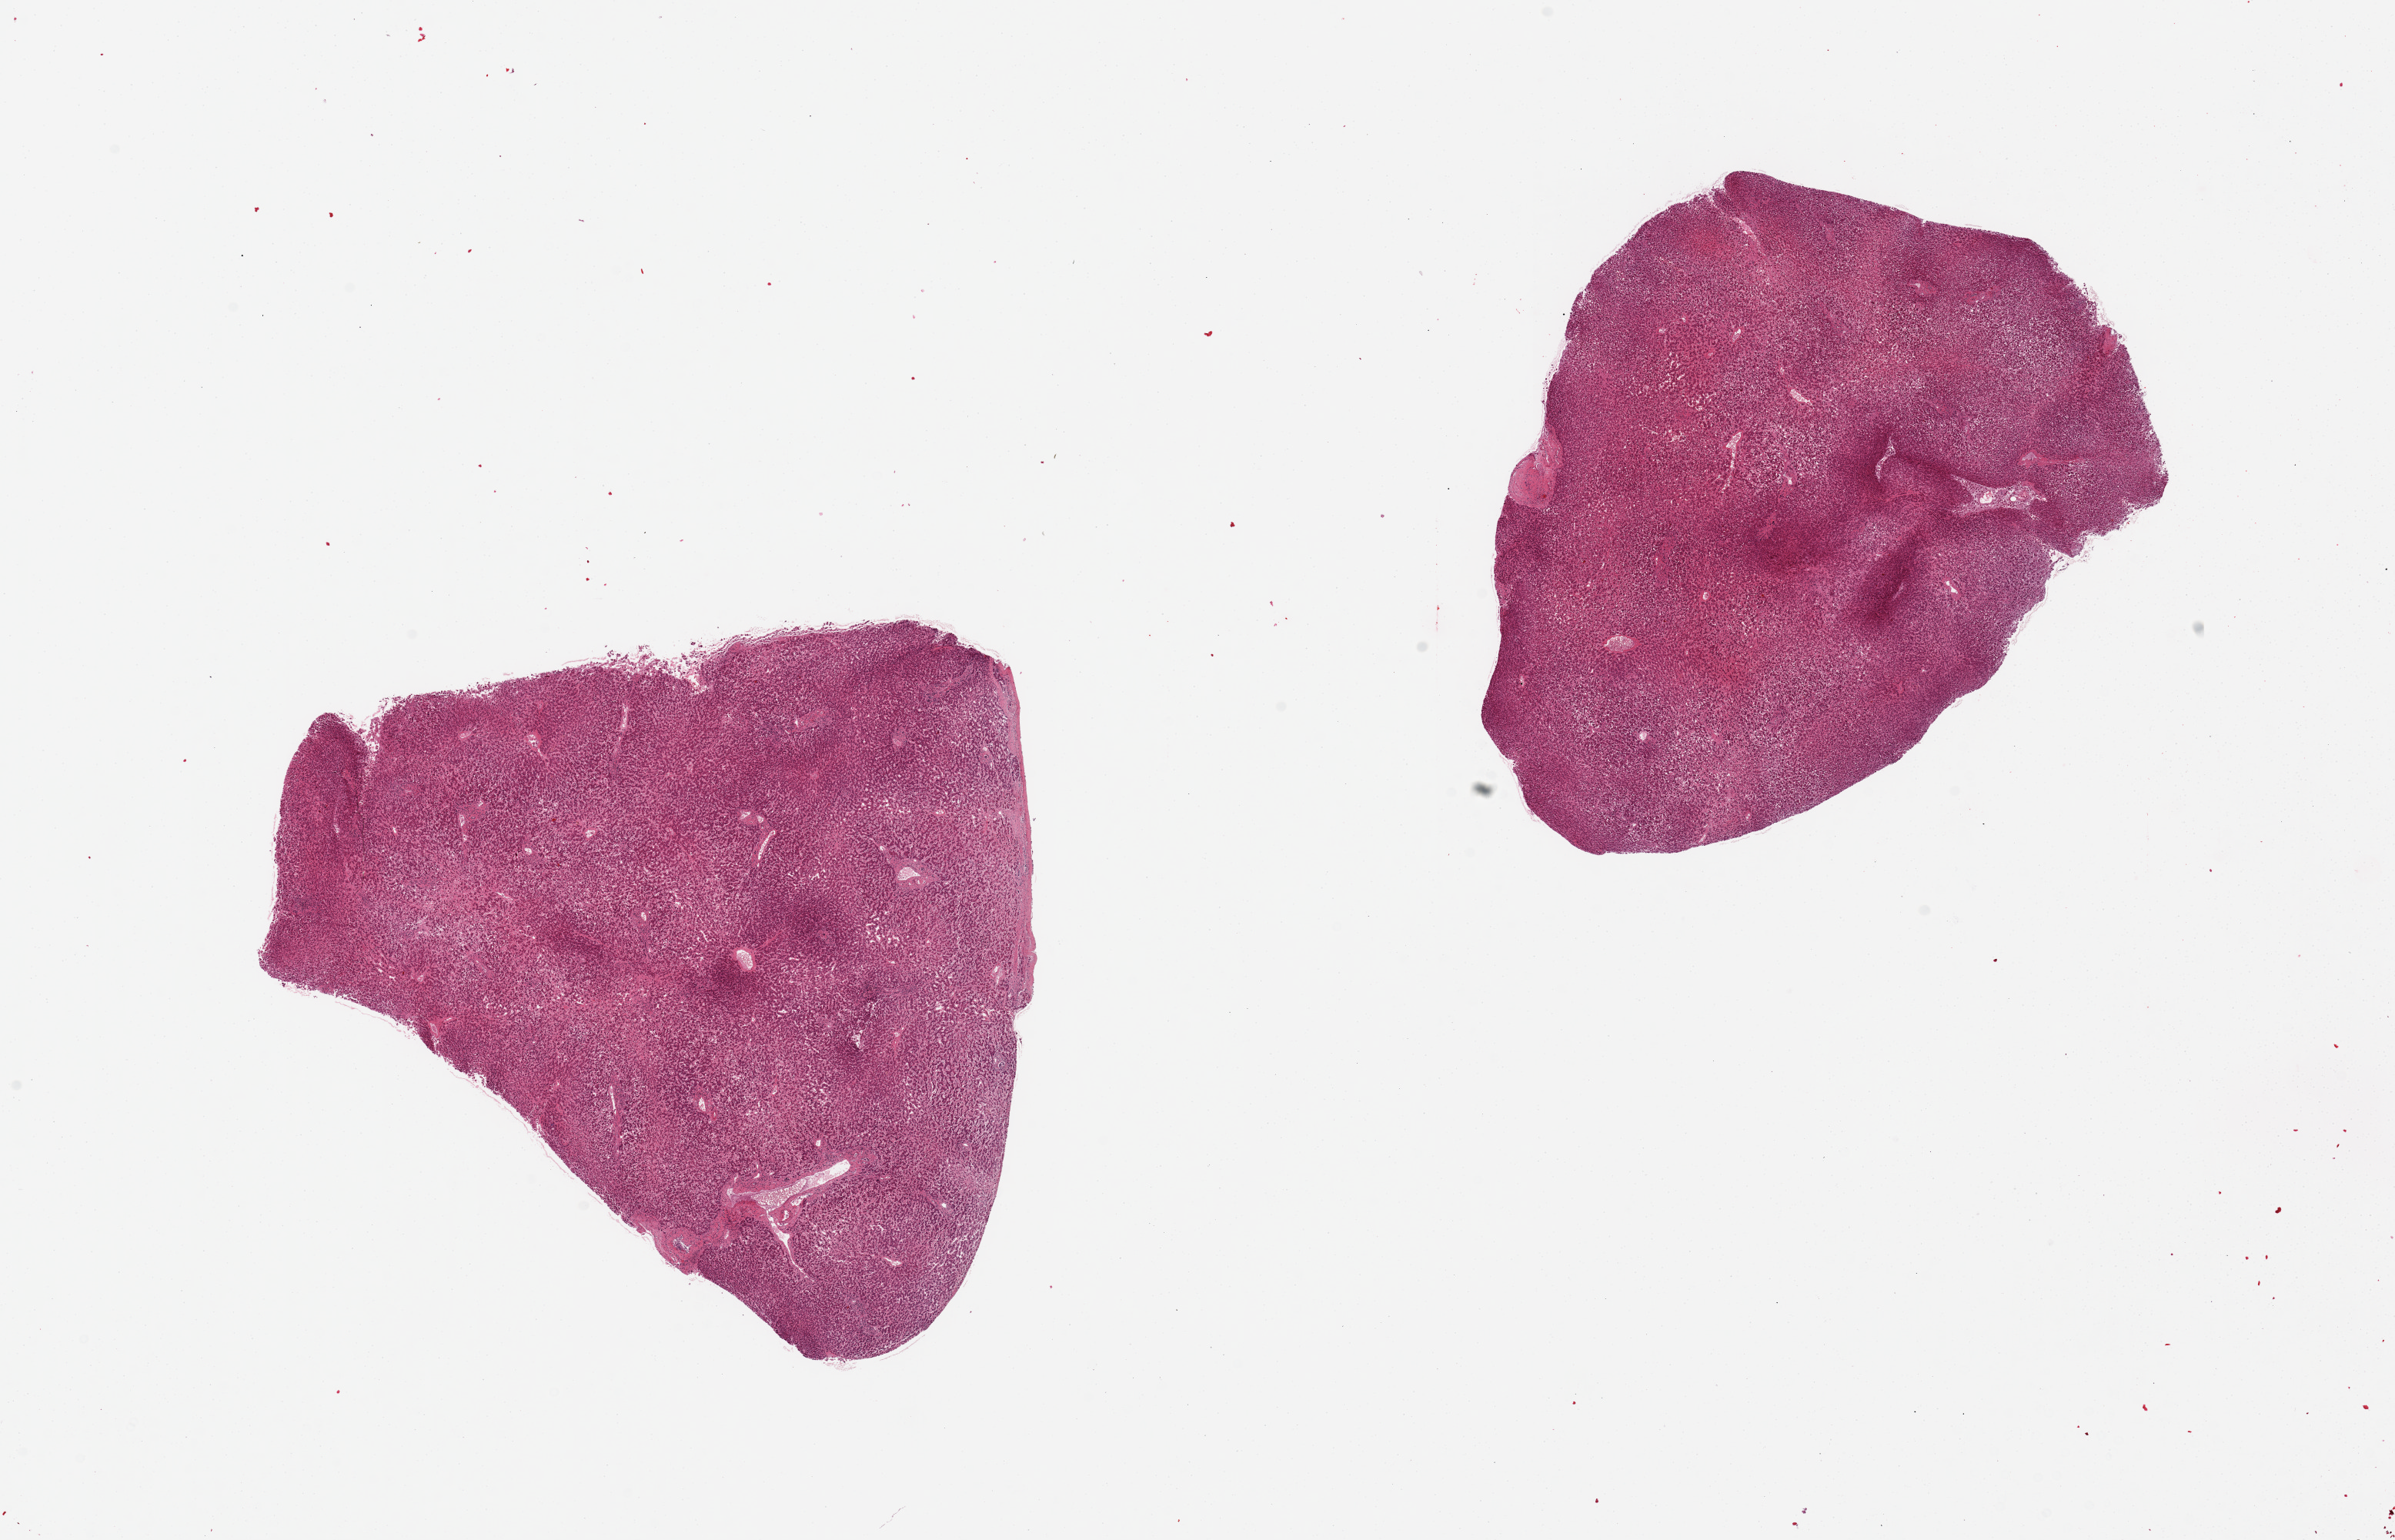
Whole-slide image, H&E stain — whole scanned area (about 24.6 x 15.8 mm, slide scanned at 20x) shown as a low-resolution overview, PAXgene-fixed paraffin-embedded (PFPE) section, sampled site (target tissue): liver, donor tissue sample. Donor: female.
* reviewer comment on this tissue sample: 2 pieces, badlyautolyzed